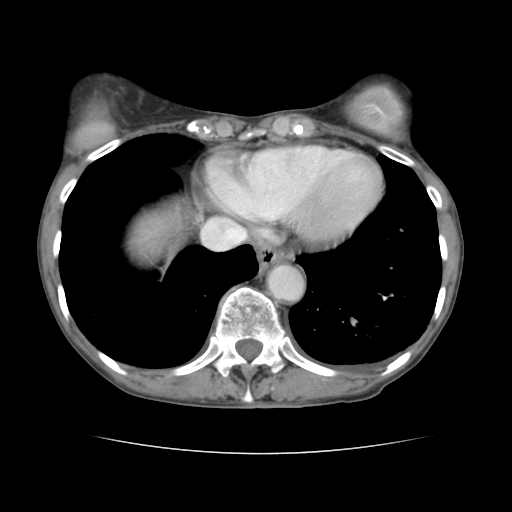
Contrast-enhanced abdominal CT, one axial slice. Slice 132 of 136 in the series (ordered by position). Intravenous contrast given. Soft-tissue window (W 400 / L 40 HU). 2.5 mm slice thickness. 512 × 512 image matrix, field of view 319 × 319 mm. Female patient, age 77 years. Case-level facts recorded for this patient, not image findings: diagnosis: colorectal cancer liver metastases, imaged before liver resection; multiple liver metastases: yes; largest metastasis: 3 cm; chemotherapy before resection: yes.
Annotated regions visible in this slice (outlined manually by an expert reader):
- hepatic veins: bounding box <202,219,247,250> (left, top, right, bottom; pixels)